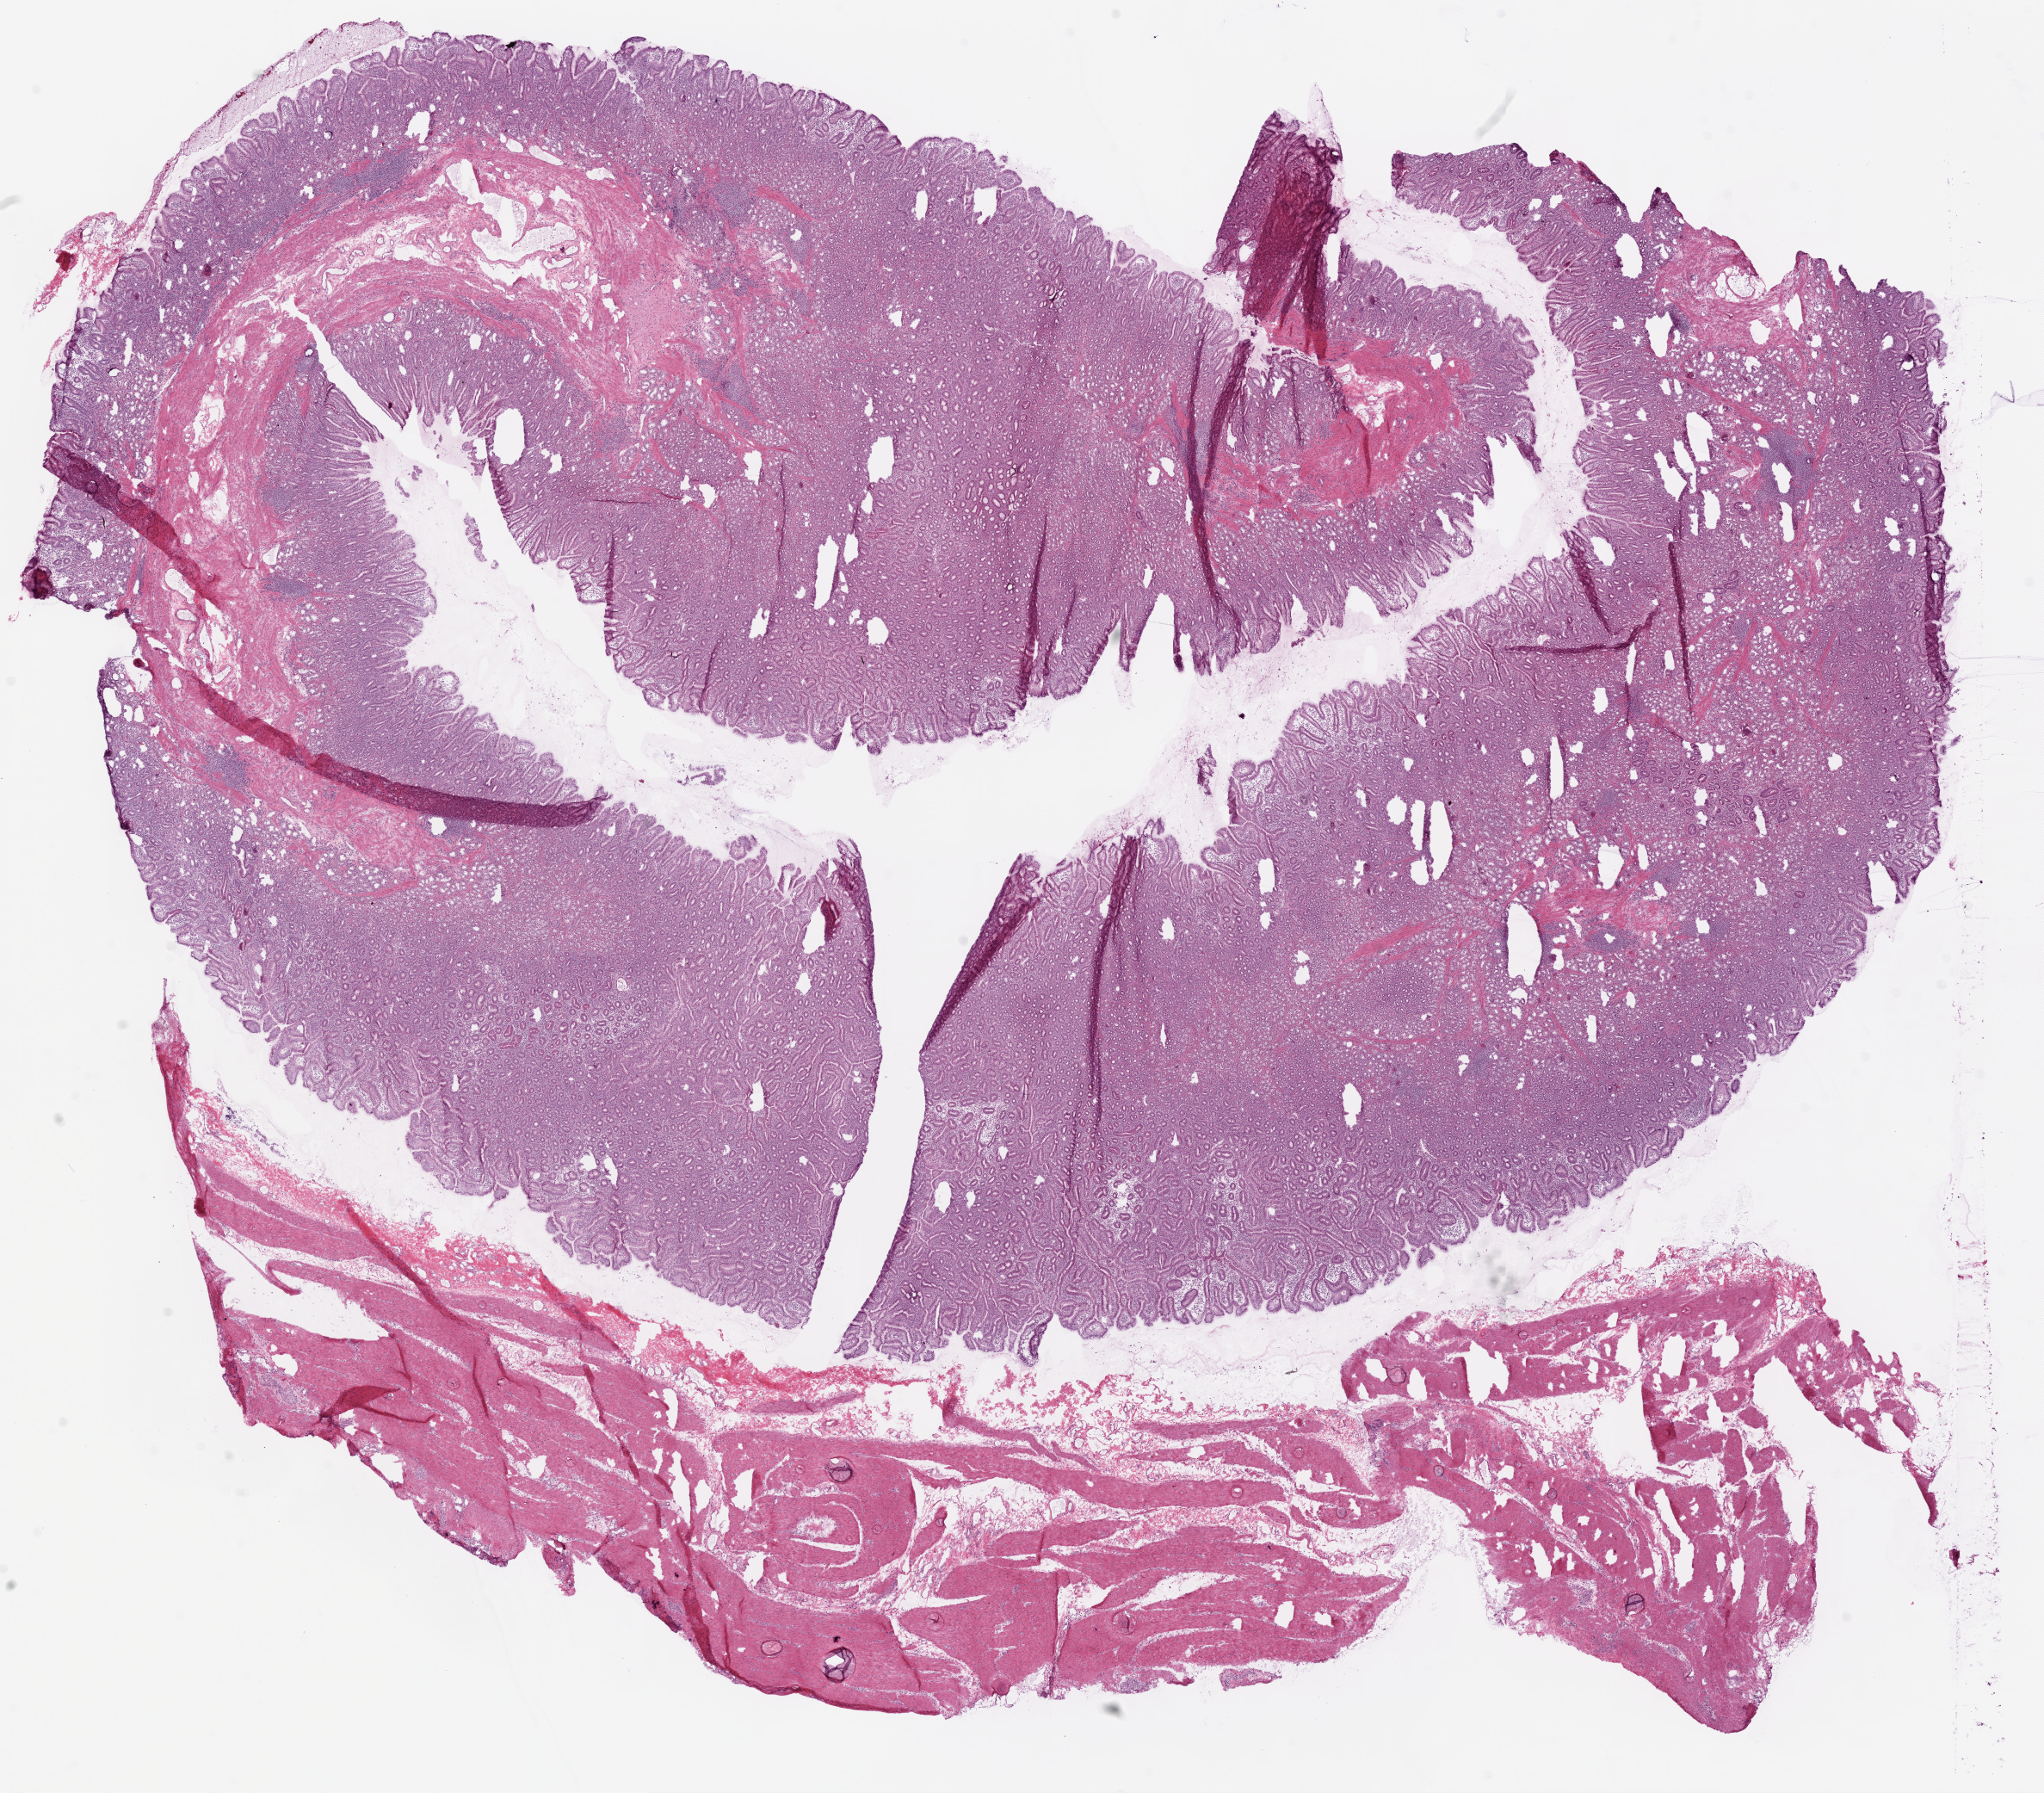
Digitized H&E-stained tissue section (whole slide) — shown as a low-resolution overview of the whole scanned area (about 19.1 x 16.7 mm, acquisition: 20x scan), frozen section from the top of the tissue portion, solid tissue normal (non-tumour tissue) sample from the stomach. Male patient; age at initial diagnosis 72 years.
* this section: solid tissue normal (non-tumour) sample from the same patient
* patient diagnosis: Adenocarcinoma, NOS